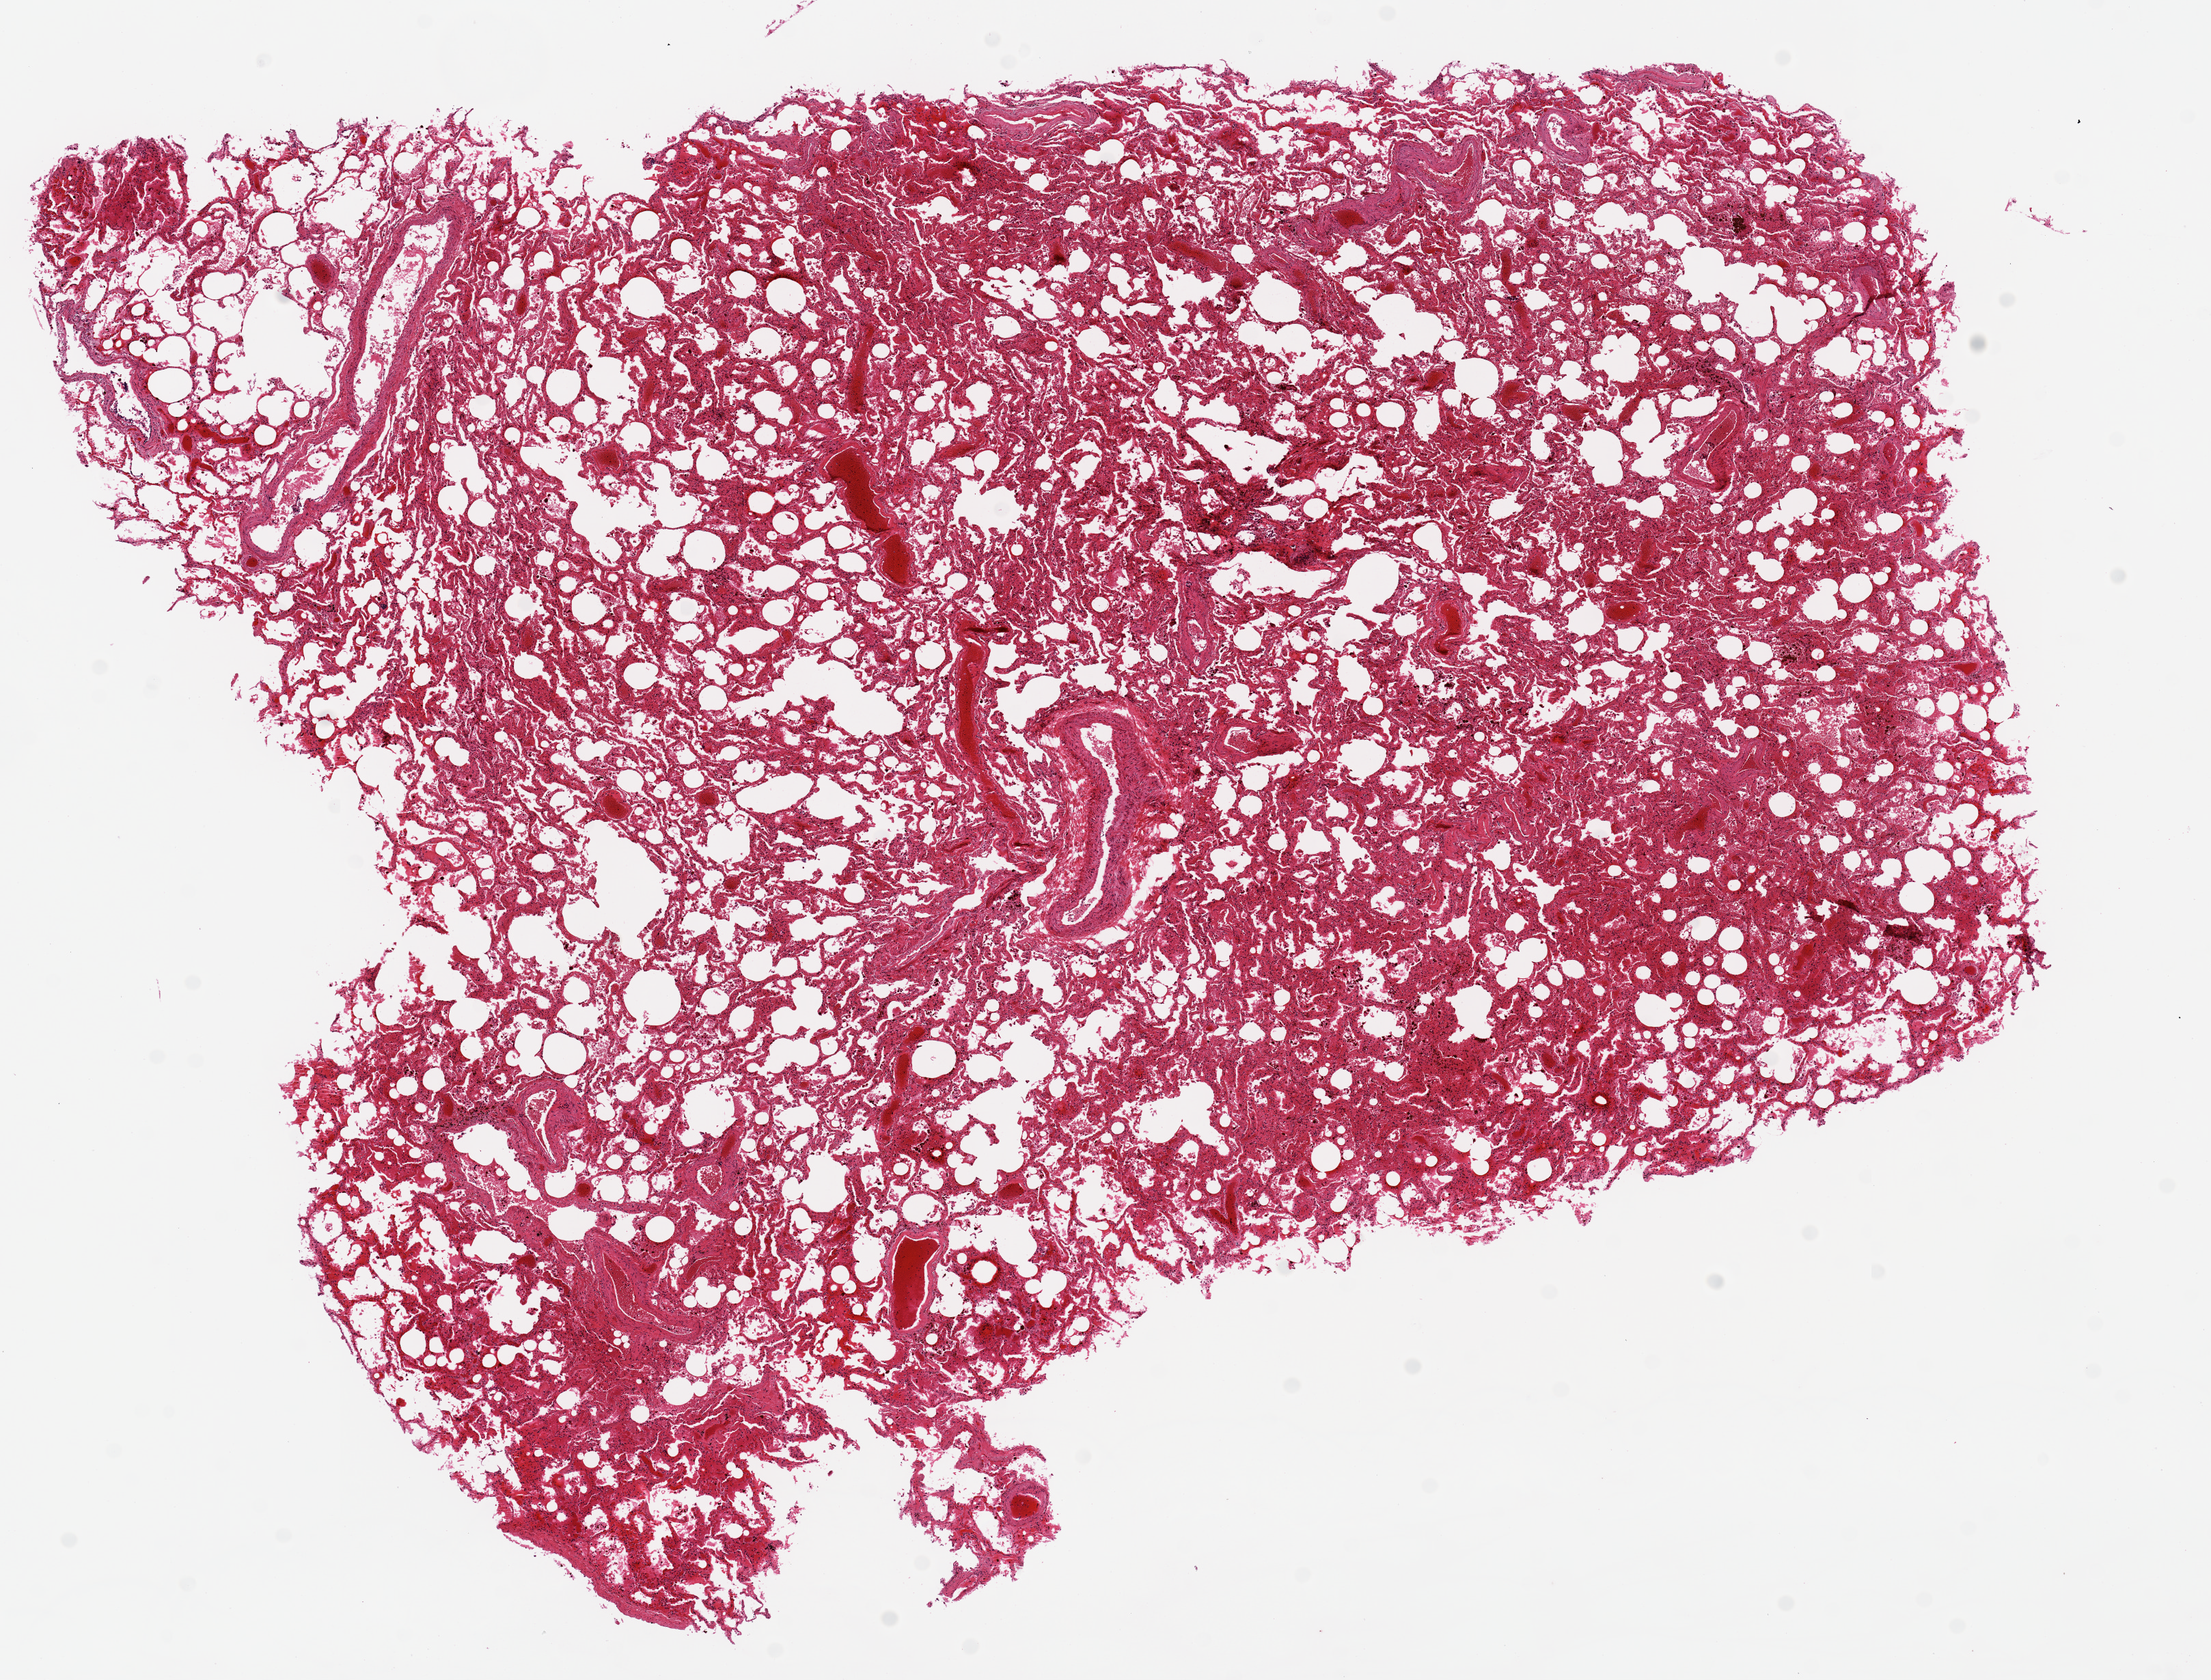
Whole-slide image, H&E stain, brightfield — a low-resolution overview of the entire scanned area, about 12.8 x 9.7 mm (acquisition: 20x scan), PAXgene-fixed, paraffin-embedded tissue, sampled site (target tissue): lung, tissue donor sample. Donor sex: female.
Review note (as recorded): Mild congestion.